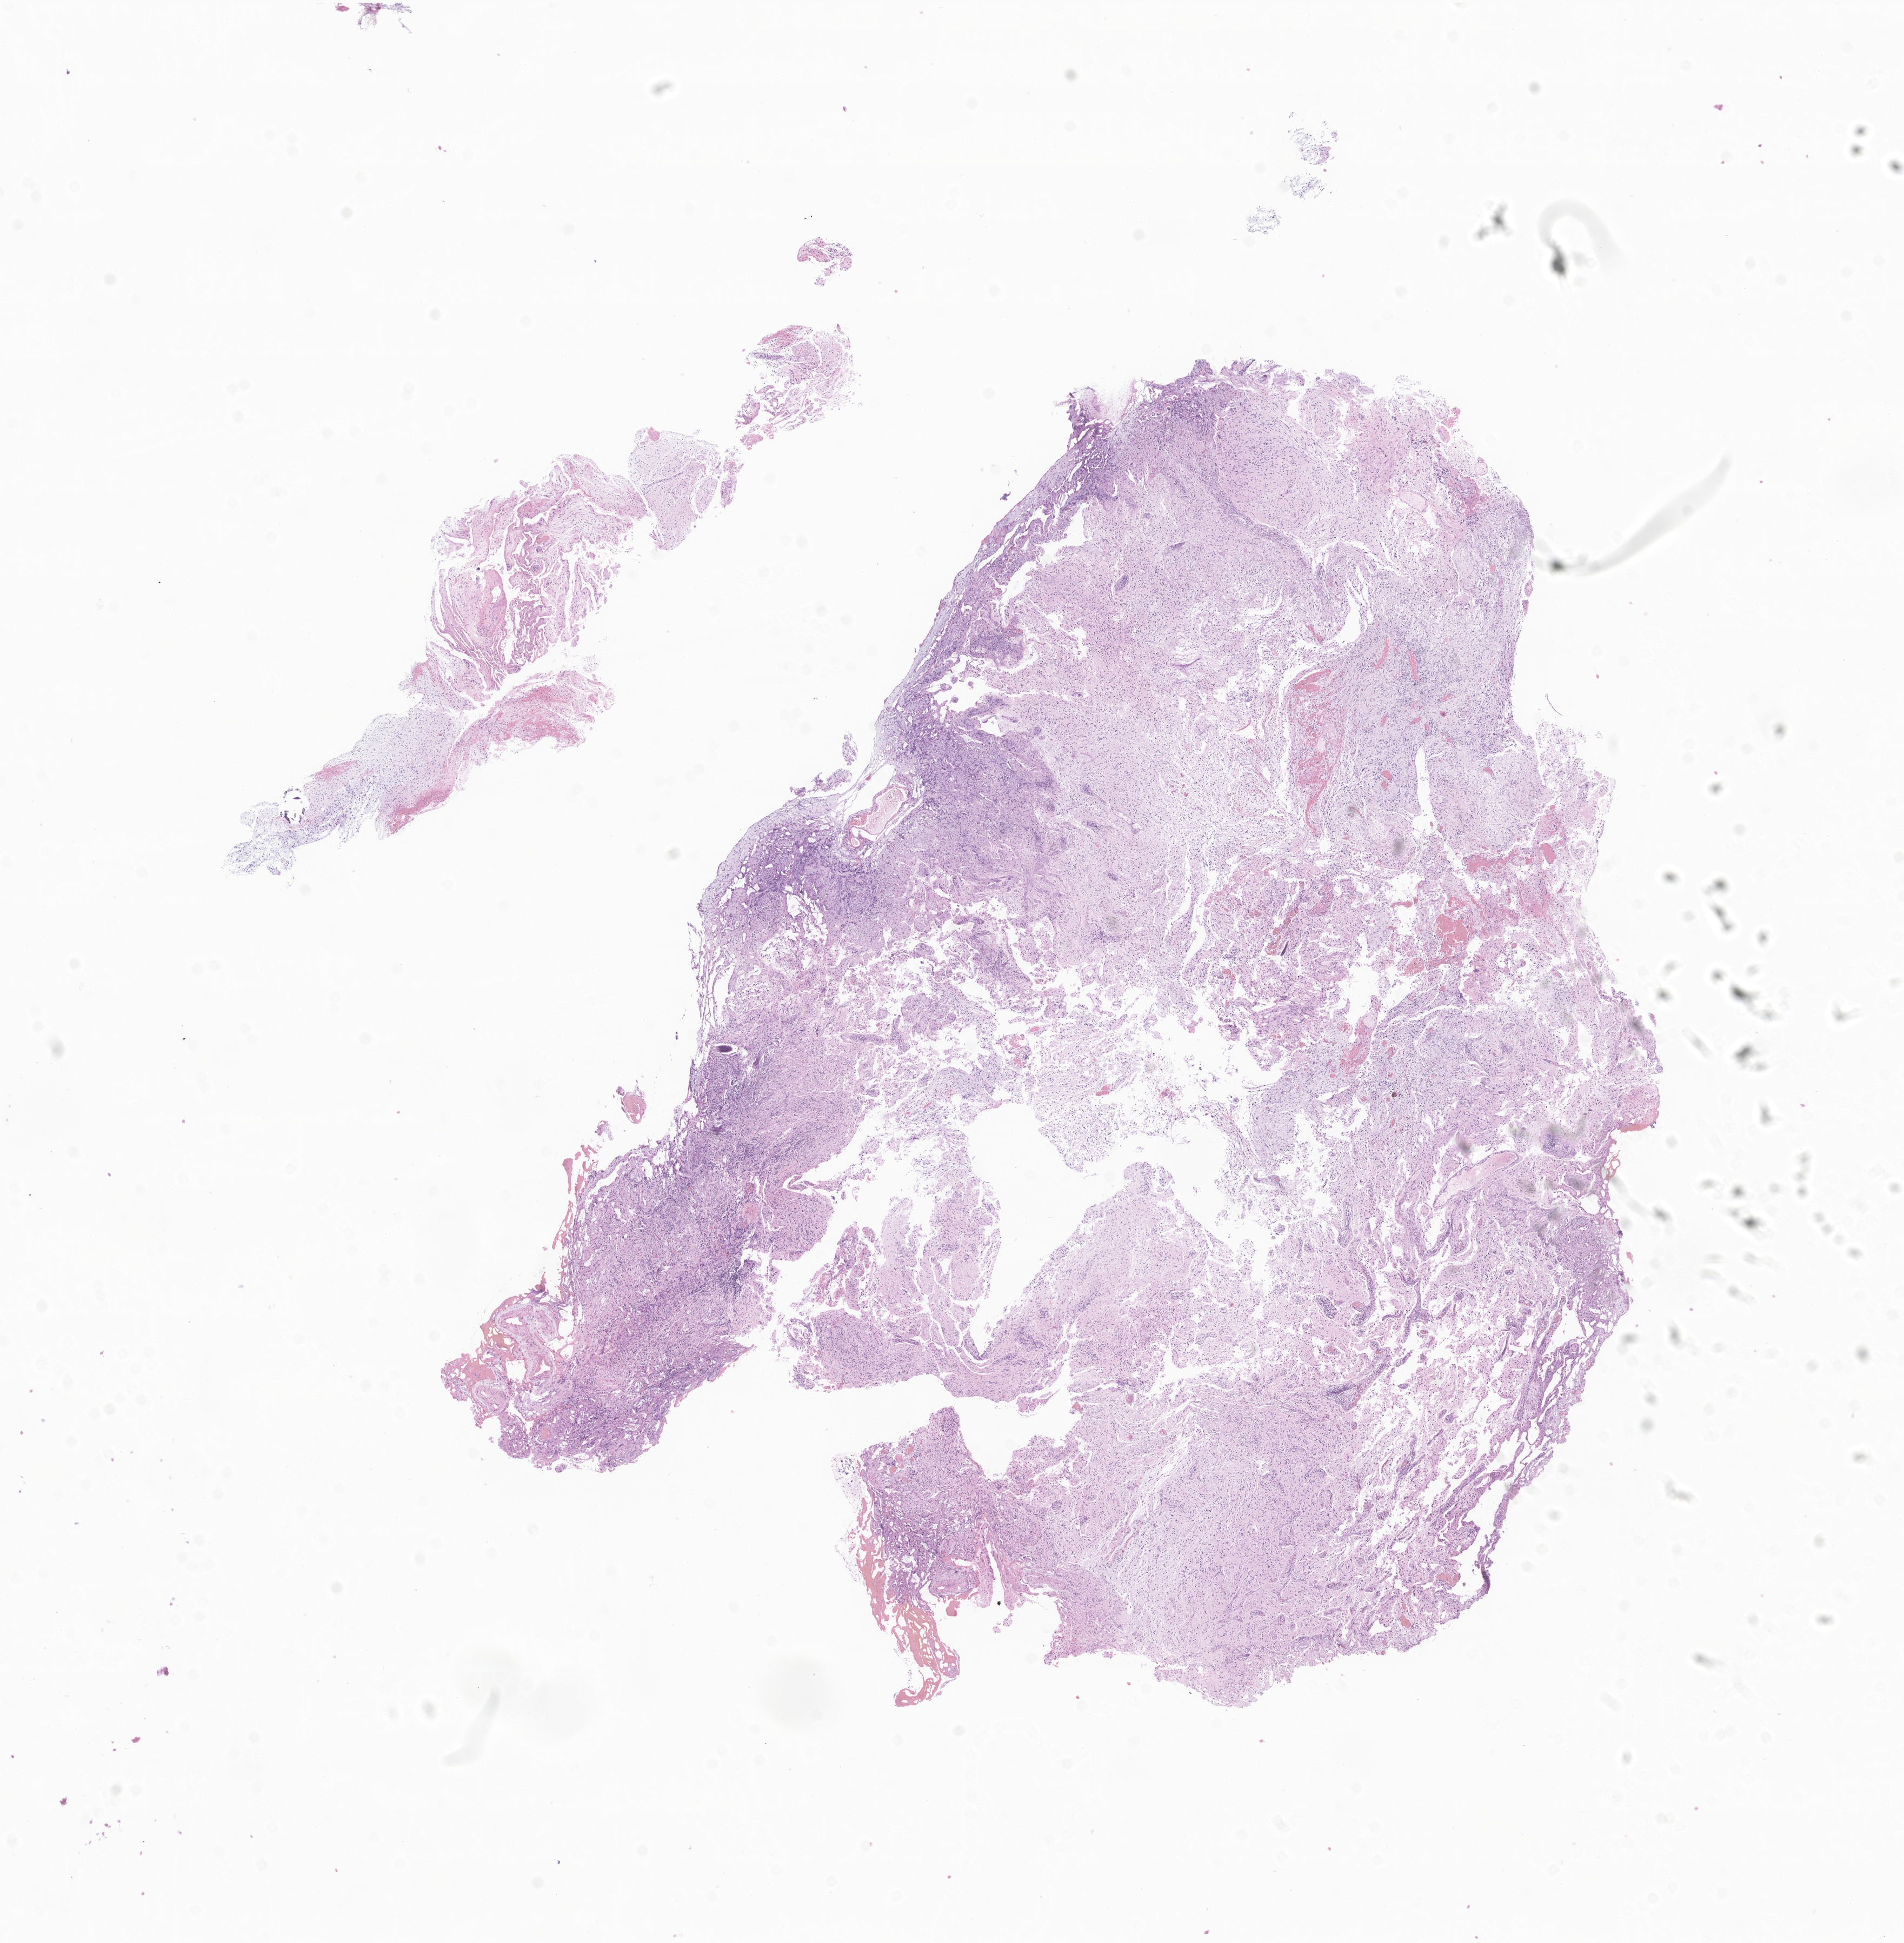
Digitized haematoxylin and eosin-stained section of tumor tissue from the brain — whole scanned area (about 14.8 x 15.2 mm) shown as a low-resolution overview. Formalin-fixed paraffin-embedded section. Patient female; age 220 months (18 years 4 months).
Recorded diagnosis: Pilocytic astrocytoma.